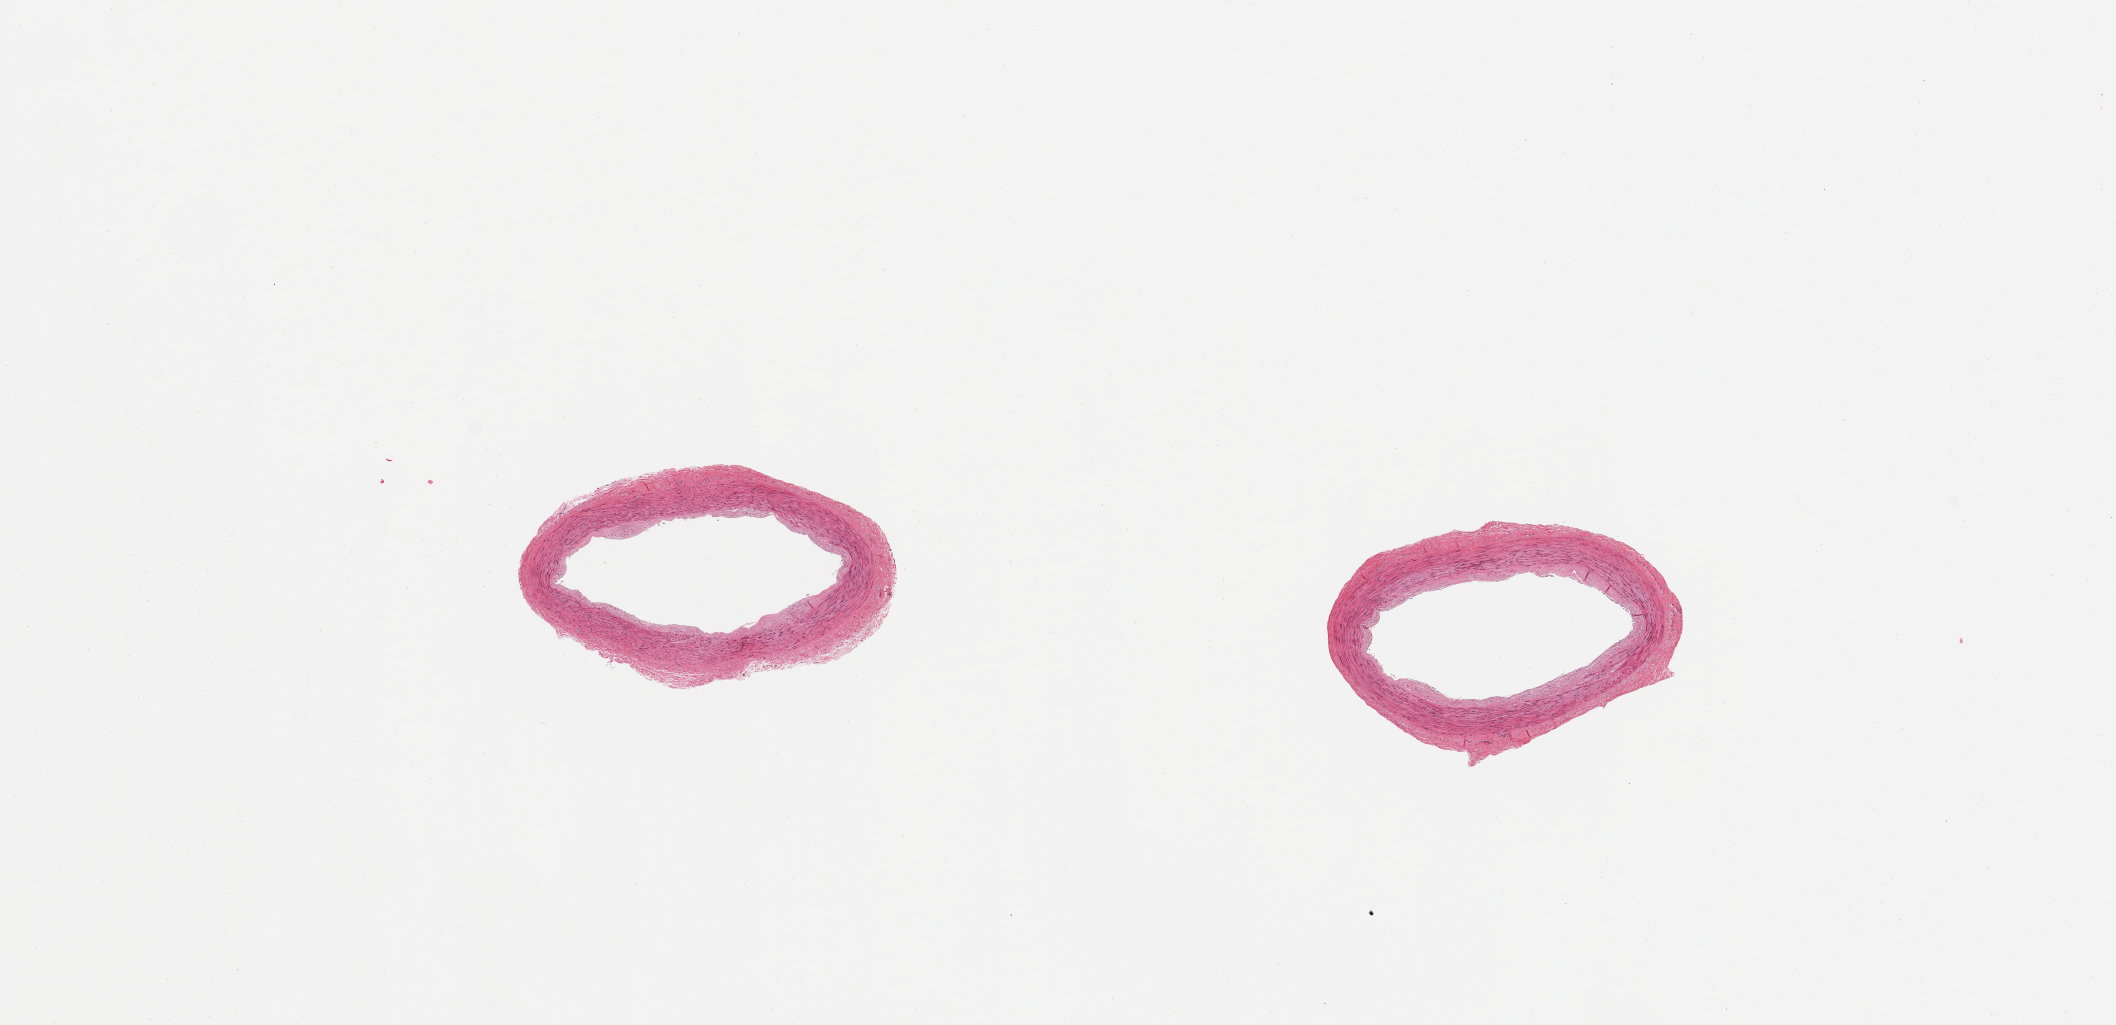
Hematoxylin and eosin (H&E) whole-slide image, brightfield, shown as a low-resolution overview of the whole scanned area (about 16.7 x 8.1 mm). PAXgene-fixed, paraffin-embedded tissue. Target tissue: tibial artery. Tissue donor sample. Donor sex: male.
- reviewer comment on this tissue sample: 2 pieces; well trimmed with mild atherosclerotic changes